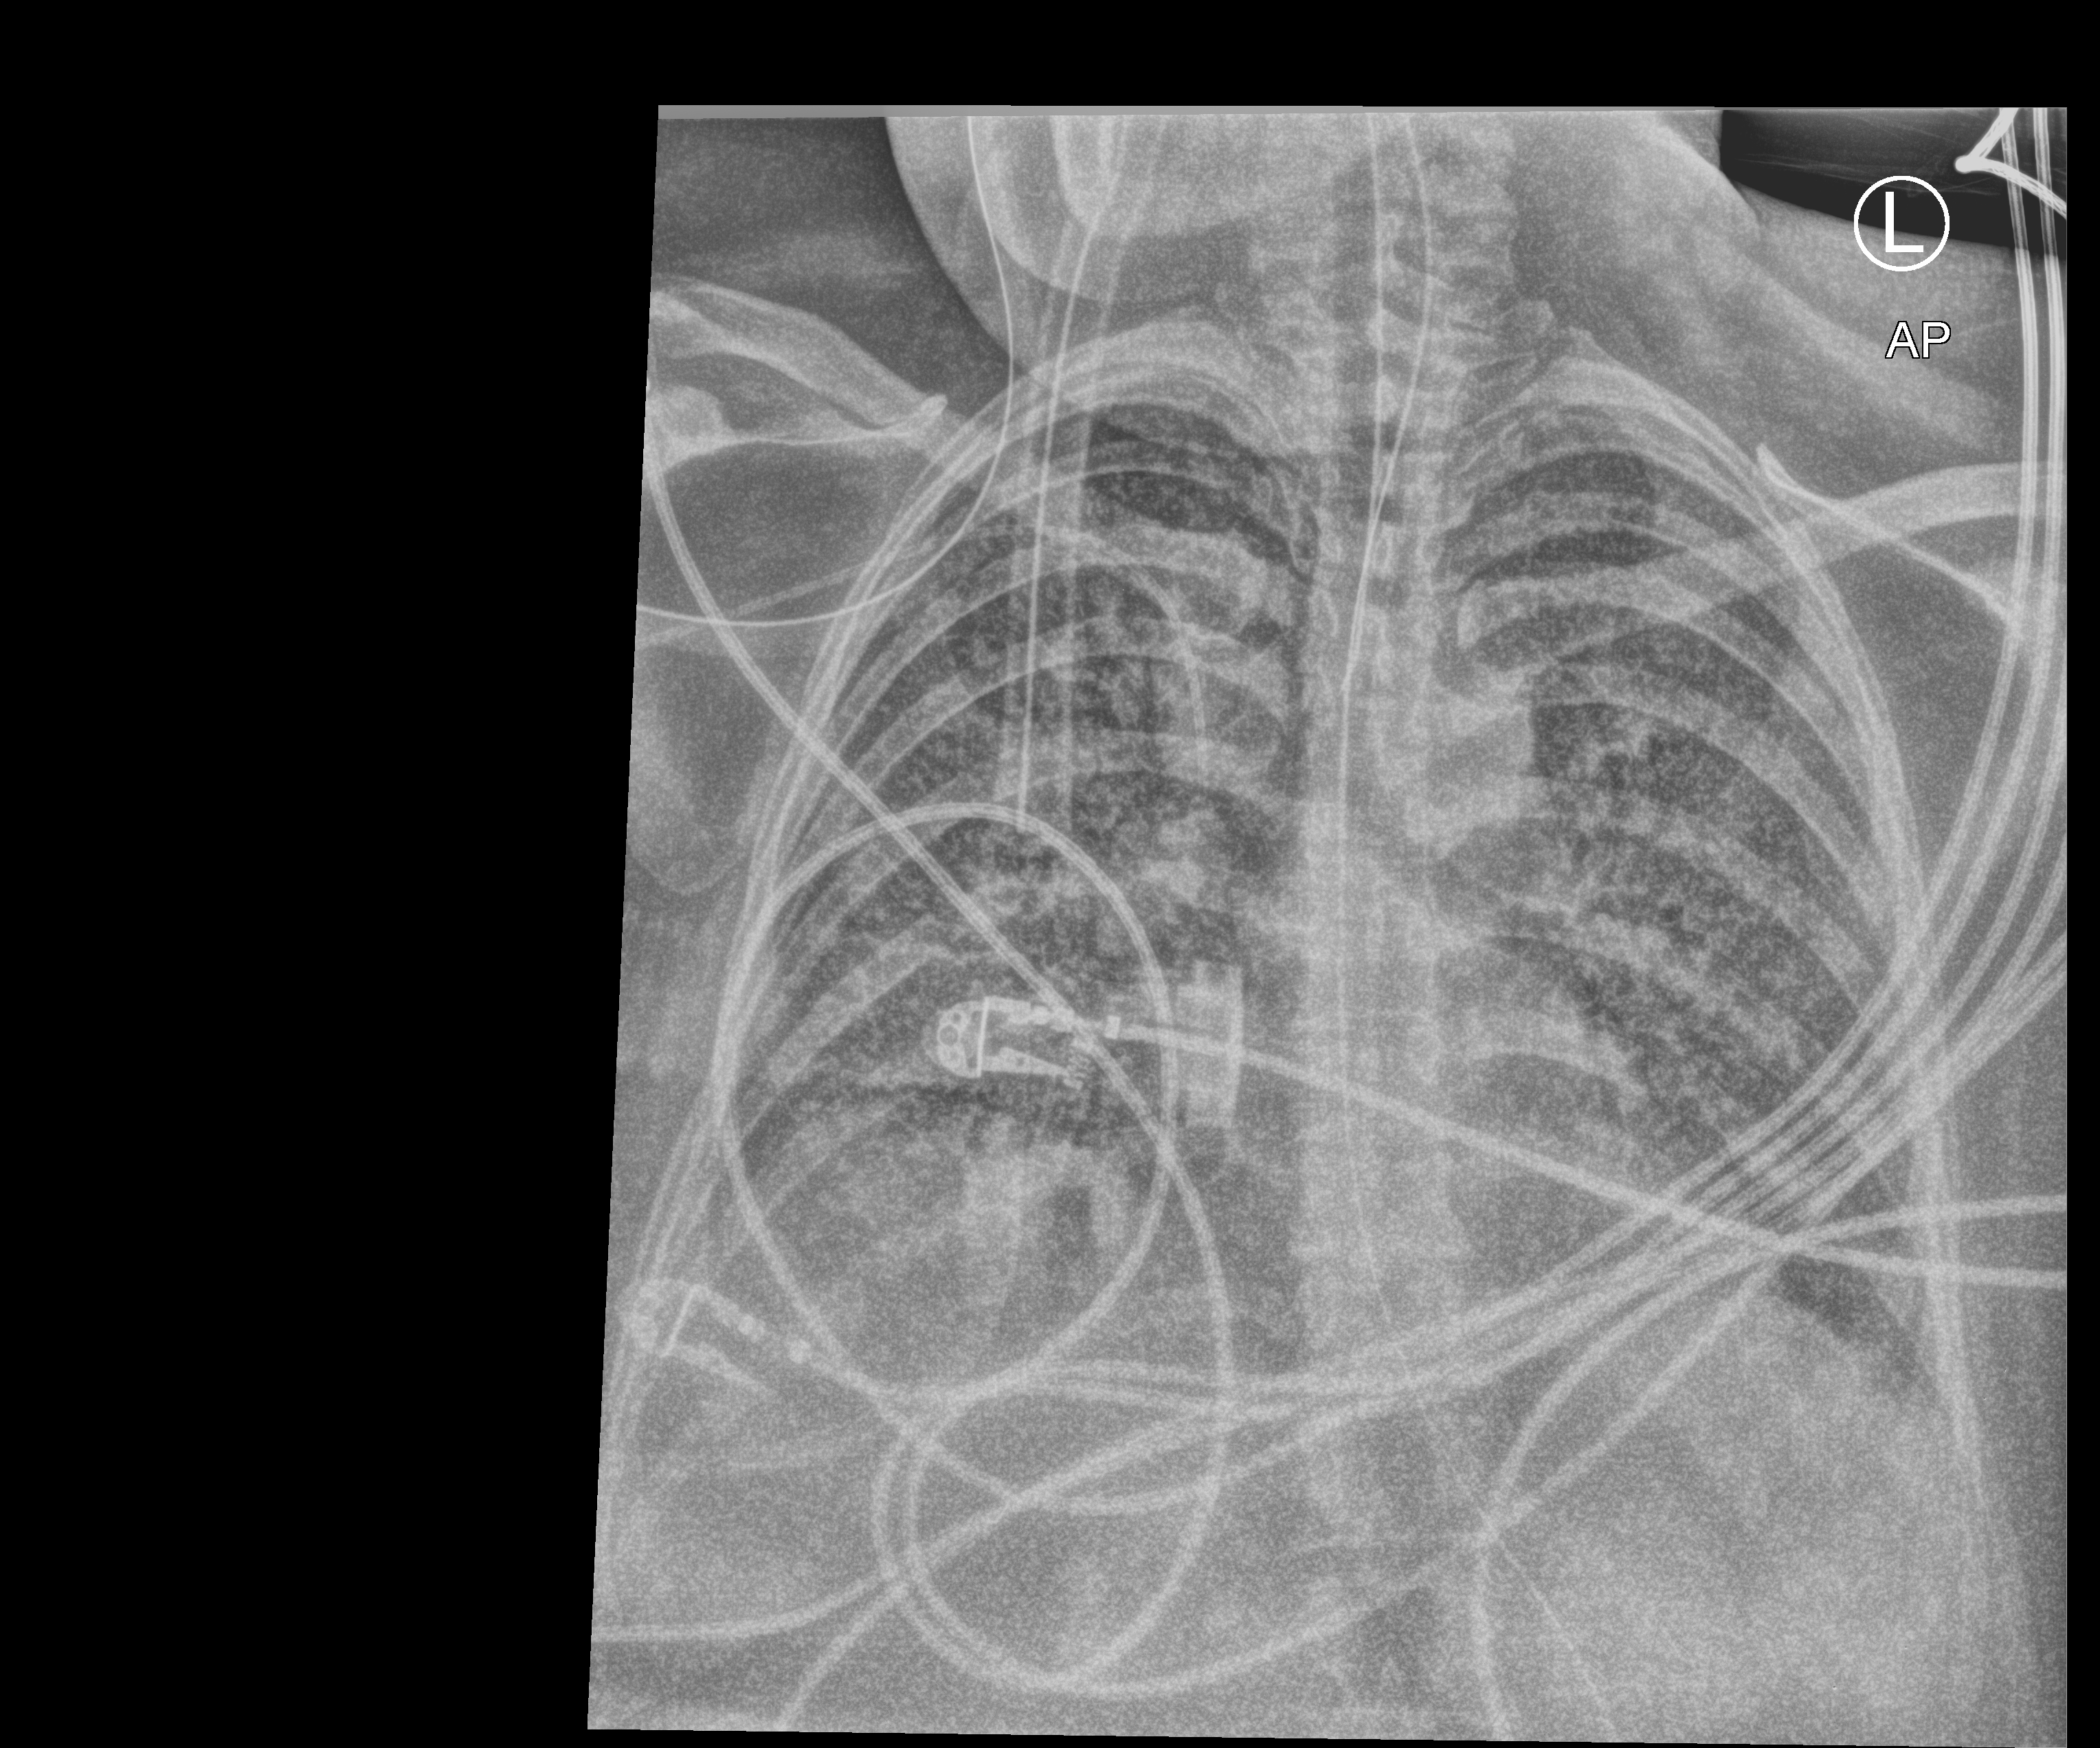
Portable chest radiograph, anteroposterior (AP) projection. Female patient hospitalised with COVID-19, age 18–59 years.
Hospital-stay facts (about this admission, not read from this image; timing relative to this image not recorded): hypertension (admission record): yes; mechanically ventilated during this hospital stay: yes.